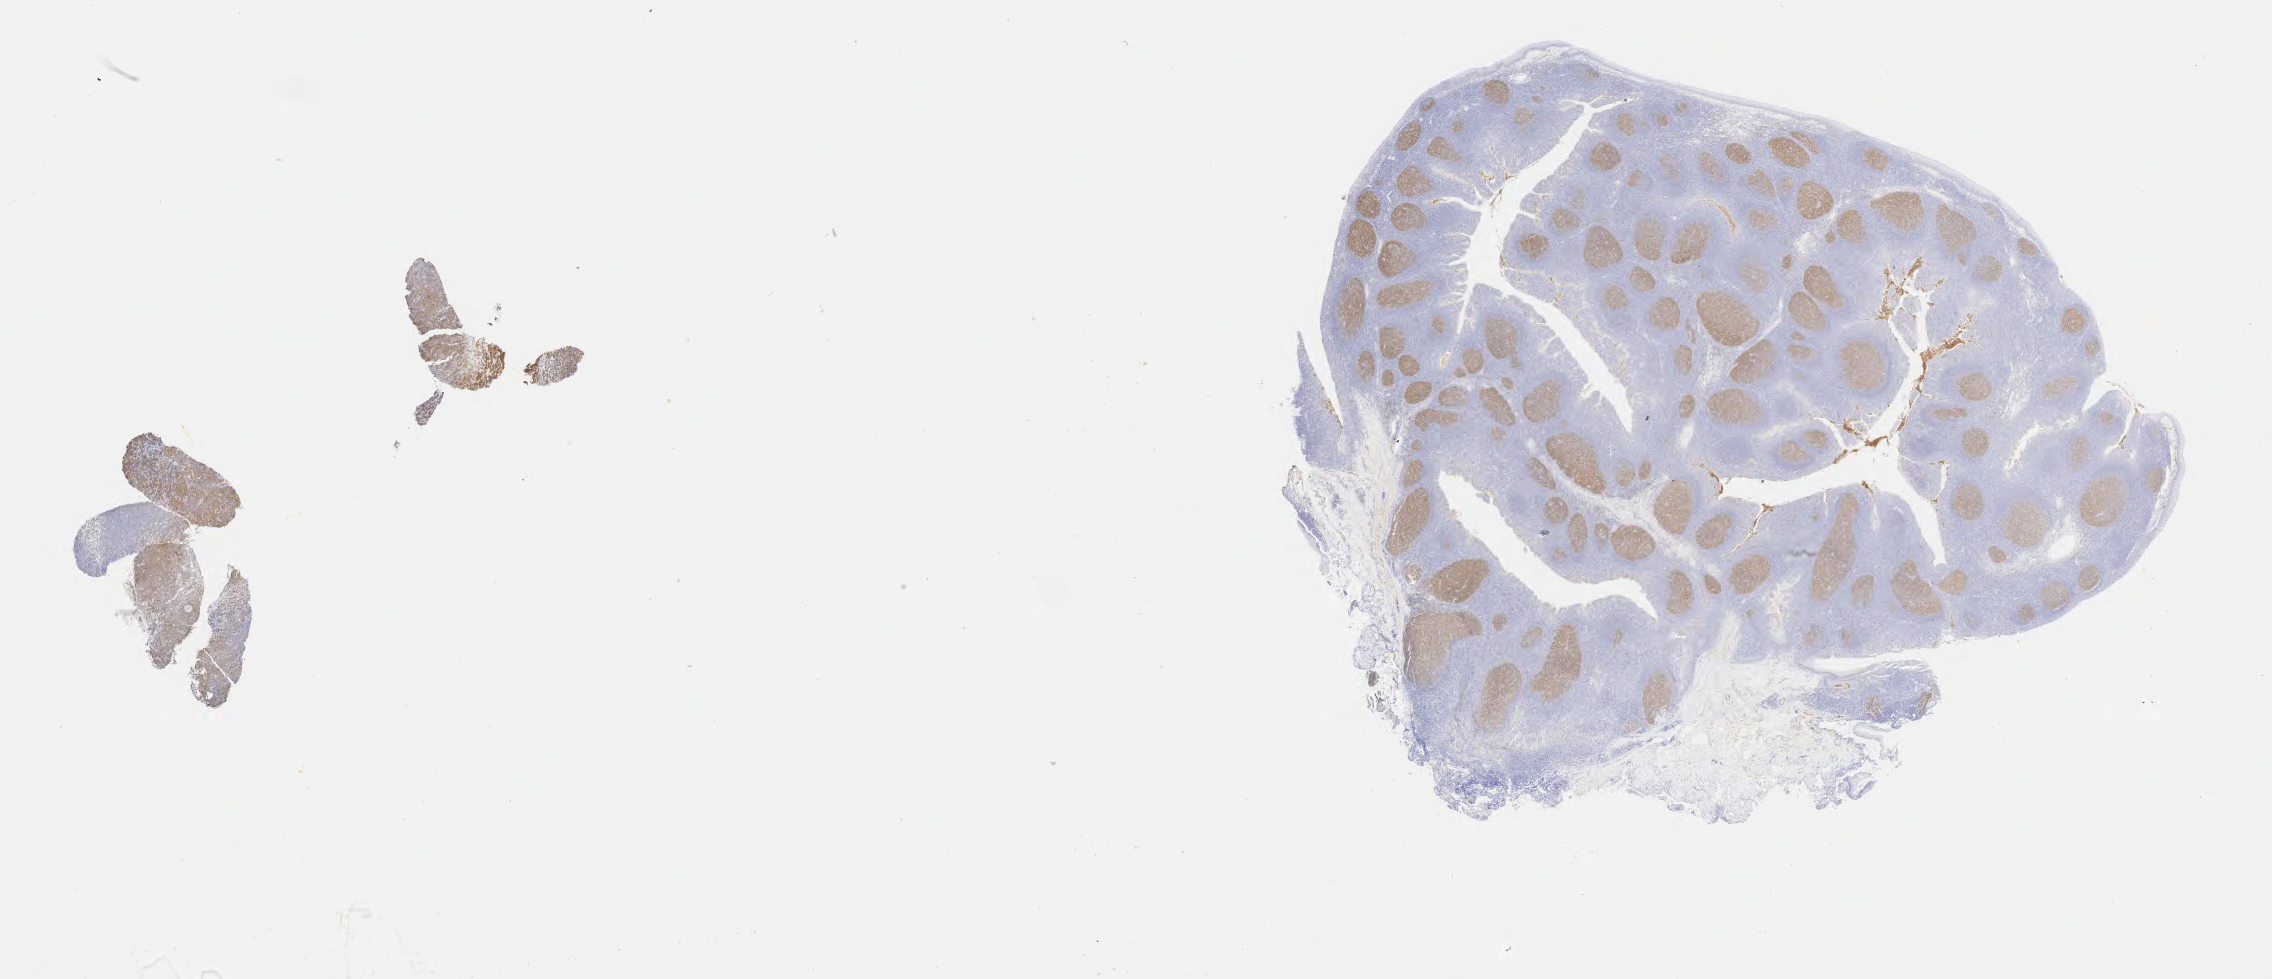
Whole-slide image, immunohistochemical stain for CD10, low-resolution overview of the scanned area, about 36.7 x 15.8 mm. Tumor tissue. Anatomic site: lymph node. Patient male; aged 54.
Histologic diagnosis: Diffuse large B-cell lymphoma, NOS.